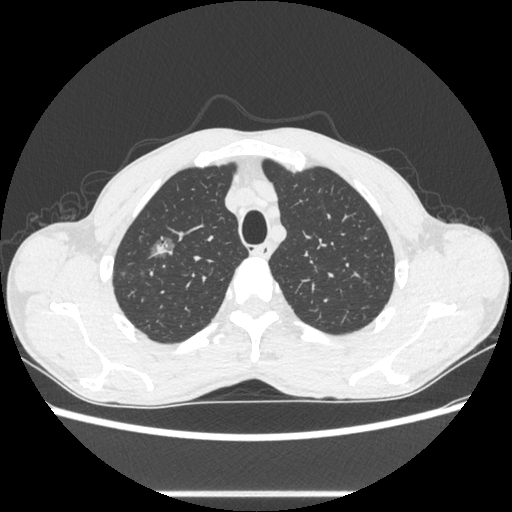
Chest CT, one axial slice. Reconstruction kernel STANDARD. 100 kVp. Lung window (W 1500 / L -600 HU). 0.62 mm slice thickness. 512 × 512 image matrix, field of view 357 × 357 mm. Male patient, age 54 years. From the clinical record (not read from this slice): clinical TNM (as recorded): T1a N0 M0.
Outlined on this slice (rectangle marked by the reading radiologist):
- lung tumour (recorded histology: adenocarcinoma): bounding box [x1, y1, x2, y2] px = [142, 229, 182, 264]